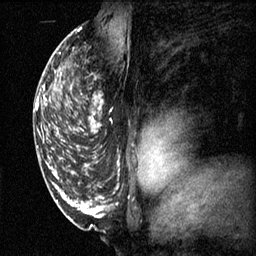
Breast MRI (dynamic contrast-enhanced), one sagittal slice; position 37 of 60 along the scan axis; 3 images stored at this slice position (order not interpretable as contrast timing); 1.5 T; TE 4.2 ms, TR 11.1 ms; 2 mm slice thickness; 256 × 256 image matrix, field of view 180 × 180 mm. Patient: female, 50 years.
Structures marked on this image (semi-automatically segmented with operator editing):
- analysis volume of interest (the breast-tissue region the enhancement analysis was run in; not a lesion): bounding box <68,68,113,141> (left, top, right, bottom; pixels)
- tumour enhancement mask (voxels above the 70 % enhancement threshold inside the analysis volume of interest): <68,94,104,135>